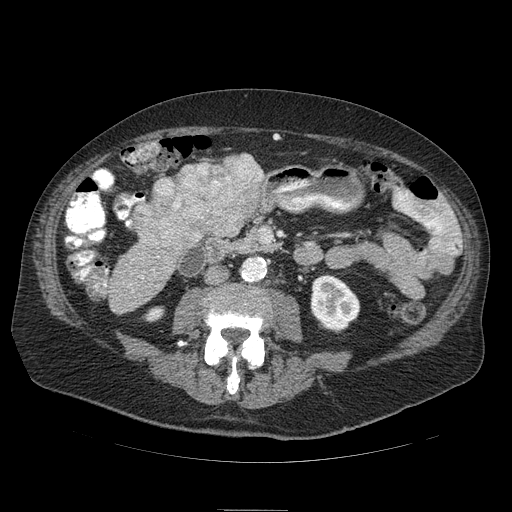
Contrast-enhanced abdominal CT (liver protocol), one axial slice; slice 17 of 103 in the series (ordered by position); 120 kVp; soft-tissue window (W 400 / L 40 HU); 2.5 mm slice thickness; 512 × 512 image matrix, field of view 440 × 440 mm. From the clinical record (not read from this slice): diagnosis: hepatocellular carcinoma (patient treated with transarterial chemoembolisation; whether this scan precedes or follows treatment is not stated here); TNM stage (as recorded): Stage-IIIA; Child-Pugh class: B; tumour differentiation: well differentiated; tumour size: 13 cm.
Outlined on this slice (semi-automatic segmentation, software-assisted and operator-edited):
- liver parenchyma outside the tumour (the mass and vessels are separate outlines, so this box may not span the whole liver): bounding box <215,154,264,196> (left, top, right, bottom; pixels)
- mass: <133,157,265,261>